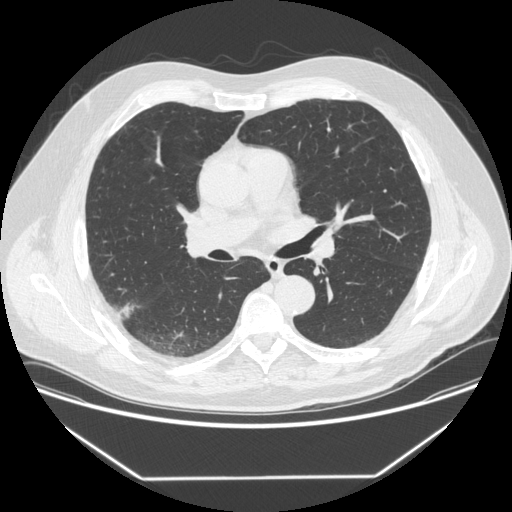
Low-dose screening chest CT, axial slice. Baseline annual screen. Lung window (W 1500 / L -600 HU). Standard (soft-tissue) reconstruction kernel (STANDARD). Slice 207 of 342 in the series. 512 × 512 image matrix. Male participant, aged 64 years at enrolment. Former smoker at enrolment.
Expert-annotated lung lesion, box from (x=100, y=298) to (x=141, y=328) px. Reader record for this screening exam (exam-level; its link to the box is not recorded): non-calcified nodule or mass ≥4 mm, right upper lobe, 12 × 12 mm, smooth margins, soft tissue attenuation. Later outcome: lung cancer diagnosed 92 days after this screen — adenocarcinoma, NOS, right upper lobe, poorly differentiated (G3), stage IIIB (AJCC 6th edition), 15 mm at pathology.